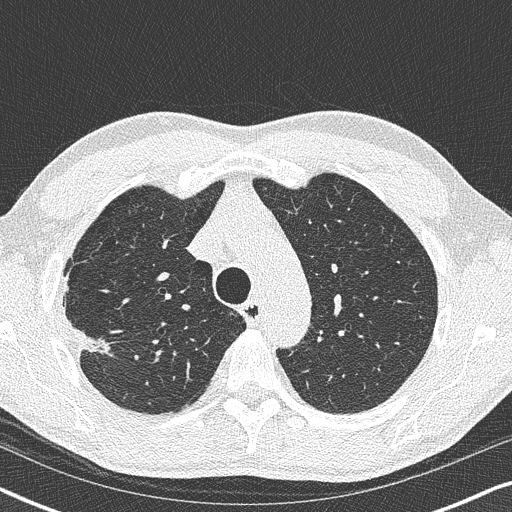
Low-dose screening chest CT, one axial slice. Position 278 of 356 along the scan axis. 120 kVp. Lung window (W 1500 / L -600 HU). 1 mm slice thickness. 512 × 512 image matrix, field of view 330 × 330 mm.
Outlined on this slice (manually delineated by an expert):
- lesion 1 (tumor, upper lobe of right lung): box from (x=73, y=326) to (x=110, y=354) px